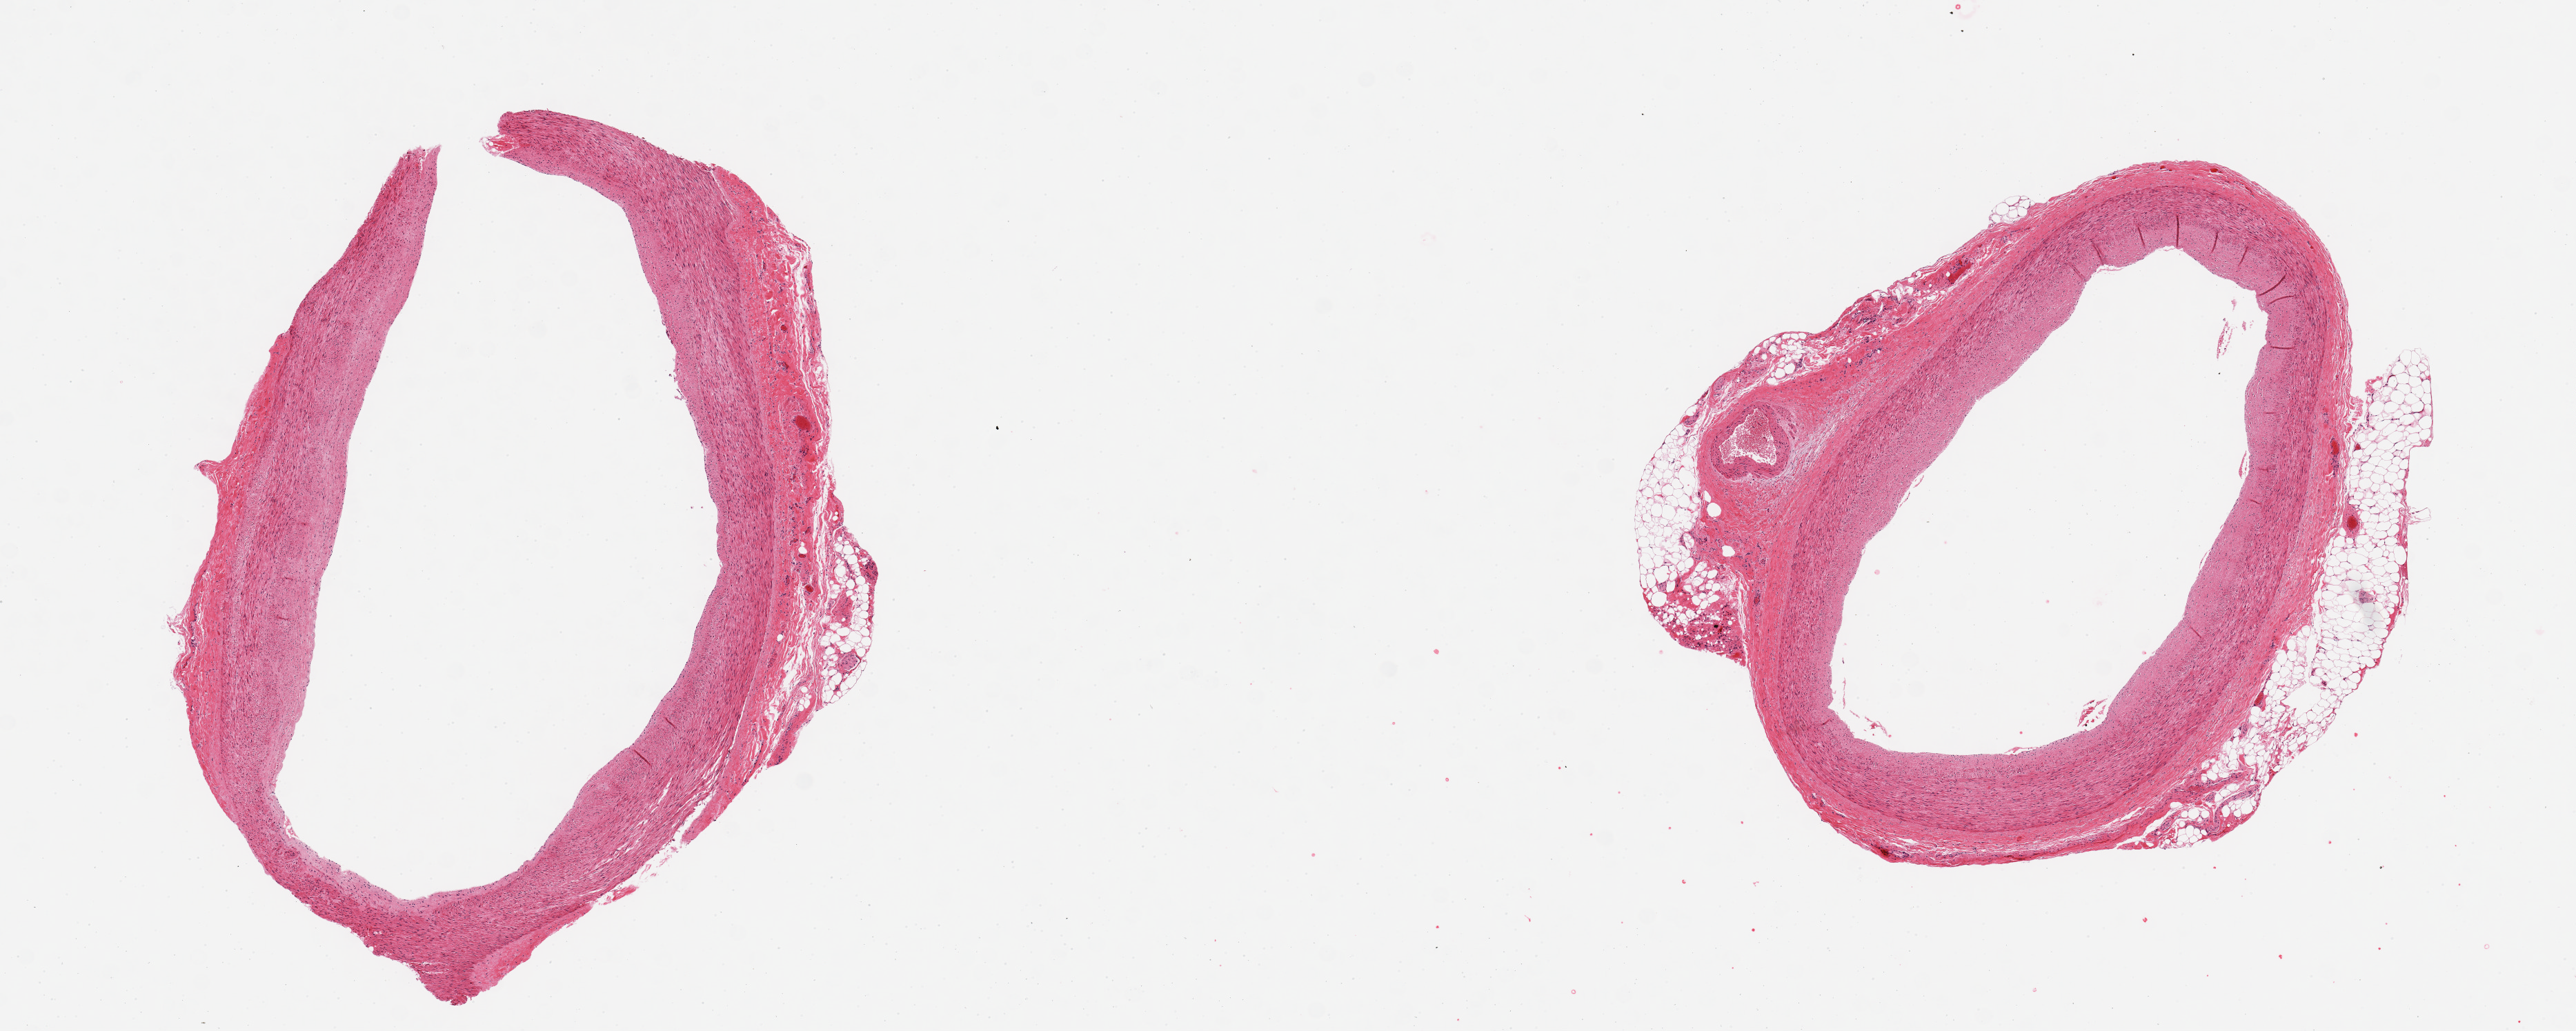
Whole-slide image, hematoxylin and eosin (H&E) stain — shown as a low-resolution overview of the whole scanned area (about 14.8 x 5.9 mm, acquisition: 20x scan), PAXgene-fixed paraffin-embedded (PFPE) section, section of coronary artery (target tissue), donor tissue sample.
• reviewer comment on this tissue sample: 2 pieces, no significant atherosis; few nubbins of adherent fat up to ~0.5mm